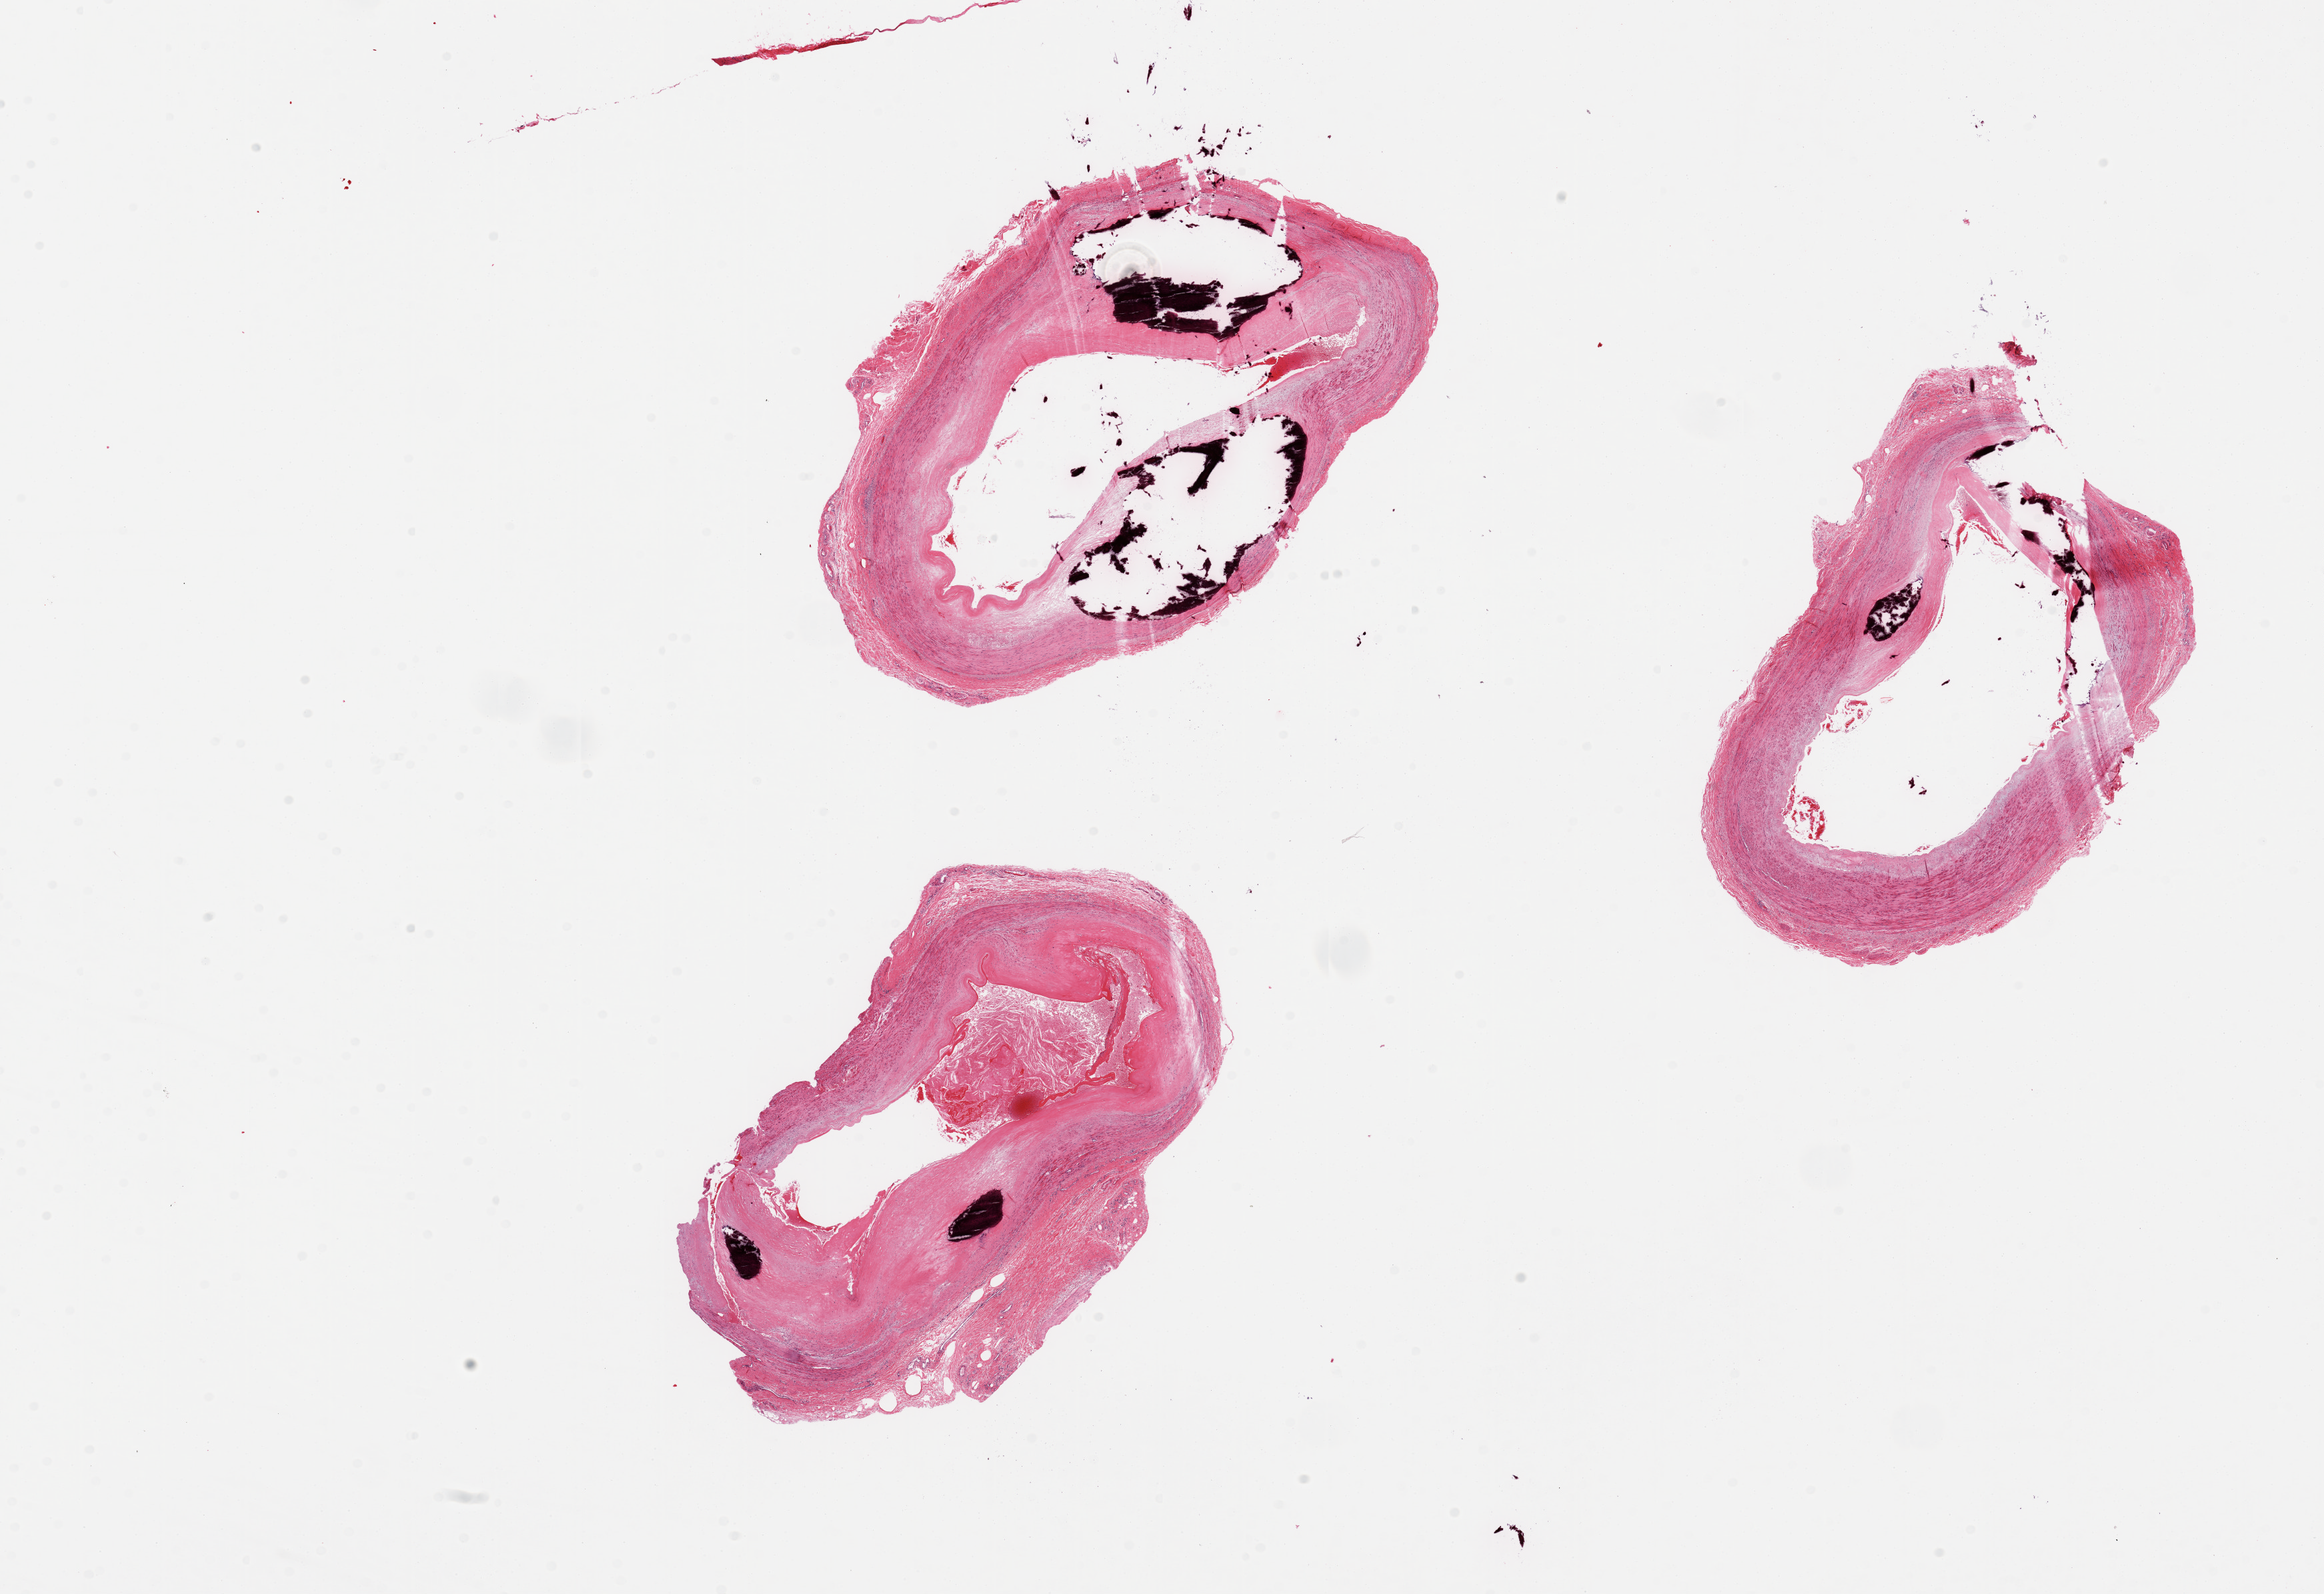
Digitized hematoxylin and eosin (H&E)-stained section, shown as a low-resolution overview of the whole scanned area (about 27.6 x 18.9 mm, slide scanned at 20x); PAXgene-fixed paraffin-embedded (PFPE) section; target tissue: tibial artery; donor tissue sample.
• reviewer comment on this tissue sample: 3 pieces; prominent calcified plaques